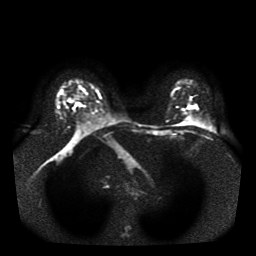
Breast MRI, one axial slice; slice 29 of 41 in the series (ordered by position); diffusion-weighted series; image 2 of 4 stored at this slice position (different b-values; order by instance number); 1.5 T; 5 mm slice thickness; 256 × 256 image matrix, field of view 330 × 330 mm. Female patient.
Outlined on this slice (expert manual segmentation):
- tumour on diffusion-weighted imaging: bounding box <72,103,85,109> (left, top, right, bottom; pixels)